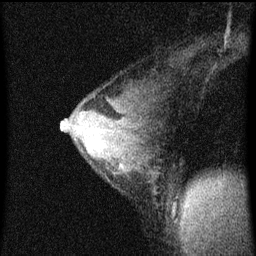
Breast MRI (dynamic contrast-enhanced), one sagittal slice; slice 40 of 60 in the series (ordered by position); dynamic contrast-enhanced series, image 2 of 4 at this slice position (ordered by acquisition); 1.5 T; TE 4.2 ms, TR 8 ms; 2 mm slice thickness; 256 × 256 image matrix, field of view 180 × 180 mm. Patient: female, 33 years.
Structures marked on this image (semi-automatic segmentation, software-assisted and operator-edited):
- analysis volume of interest (the breast-tissue region the enhancement analysis was run in; not a lesion): box from (x=62, y=82) to (x=171, y=217) px
- tumour enhancement mask (voxels above the 70 % enhancement threshold inside the analysis volume of interest): (x=62, y=122)–(x=87, y=151)